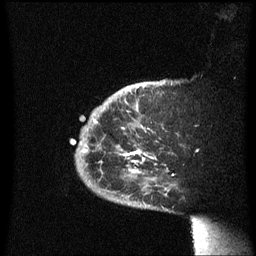
Breast MRI (dynamic contrast-enhanced), one sagittal slice. Slice 50 of 60 in the series (ordered by position). Dynamic contrast-enhanced series, image 2 of 3 at this slice position (ordered by acquisition). 1.5 T. TE 4.2 ms, TR 8.4 ms. 2.3 mm slice thickness. 256 × 256 image matrix. Female patient, age 38 years. Case-level facts recorded for this patient, not image findings: setting: breast cancer imaged before/during neoadjuvant chemotherapy; receptor status: HER2-positive.
Annotated regions visible in this slice (semi-automatic segmentation, software-assisted and operator-edited):
- analysis volume of interest (the breast-tissue region the enhancement analysis was run in; not a lesion): bounding box (x1, y1, x2, y2) in pixels: (70, 80, 182, 211)
- tumour enhancement mask (voxels above the 70 % enhancement threshold inside the analysis volume of interest): (94, 120, 154, 173)